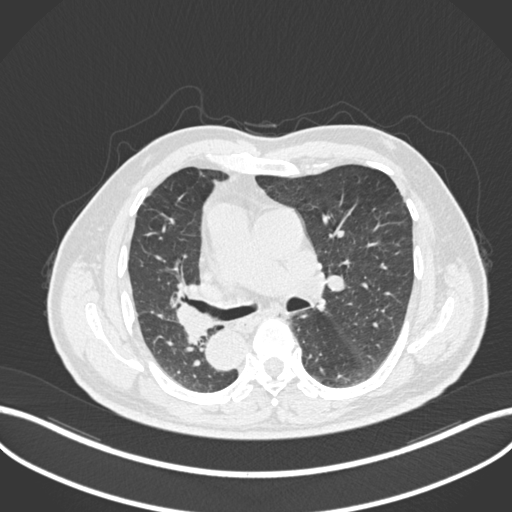
Chest CT, one axial slice; slice 129 of 206 in the series (ordered by position); reconstruction kernel B30f; 120 kVp; lung window (W 1500 / L -600 HU); 1 mm slice thickness; 512 × 512 image matrix. Male patient, age 67 years. Case-level facts recorded for this patient, not image findings: clinical TNM (as recorded): T2a N0 M0.
Outlined on this slice (bounding box drawn by a radiologist):
- lung tumour (recorded histology: squamous cell carcinoma): bounding box (x1, y1, x2, y2) in pixels: (165, 293, 212, 350)